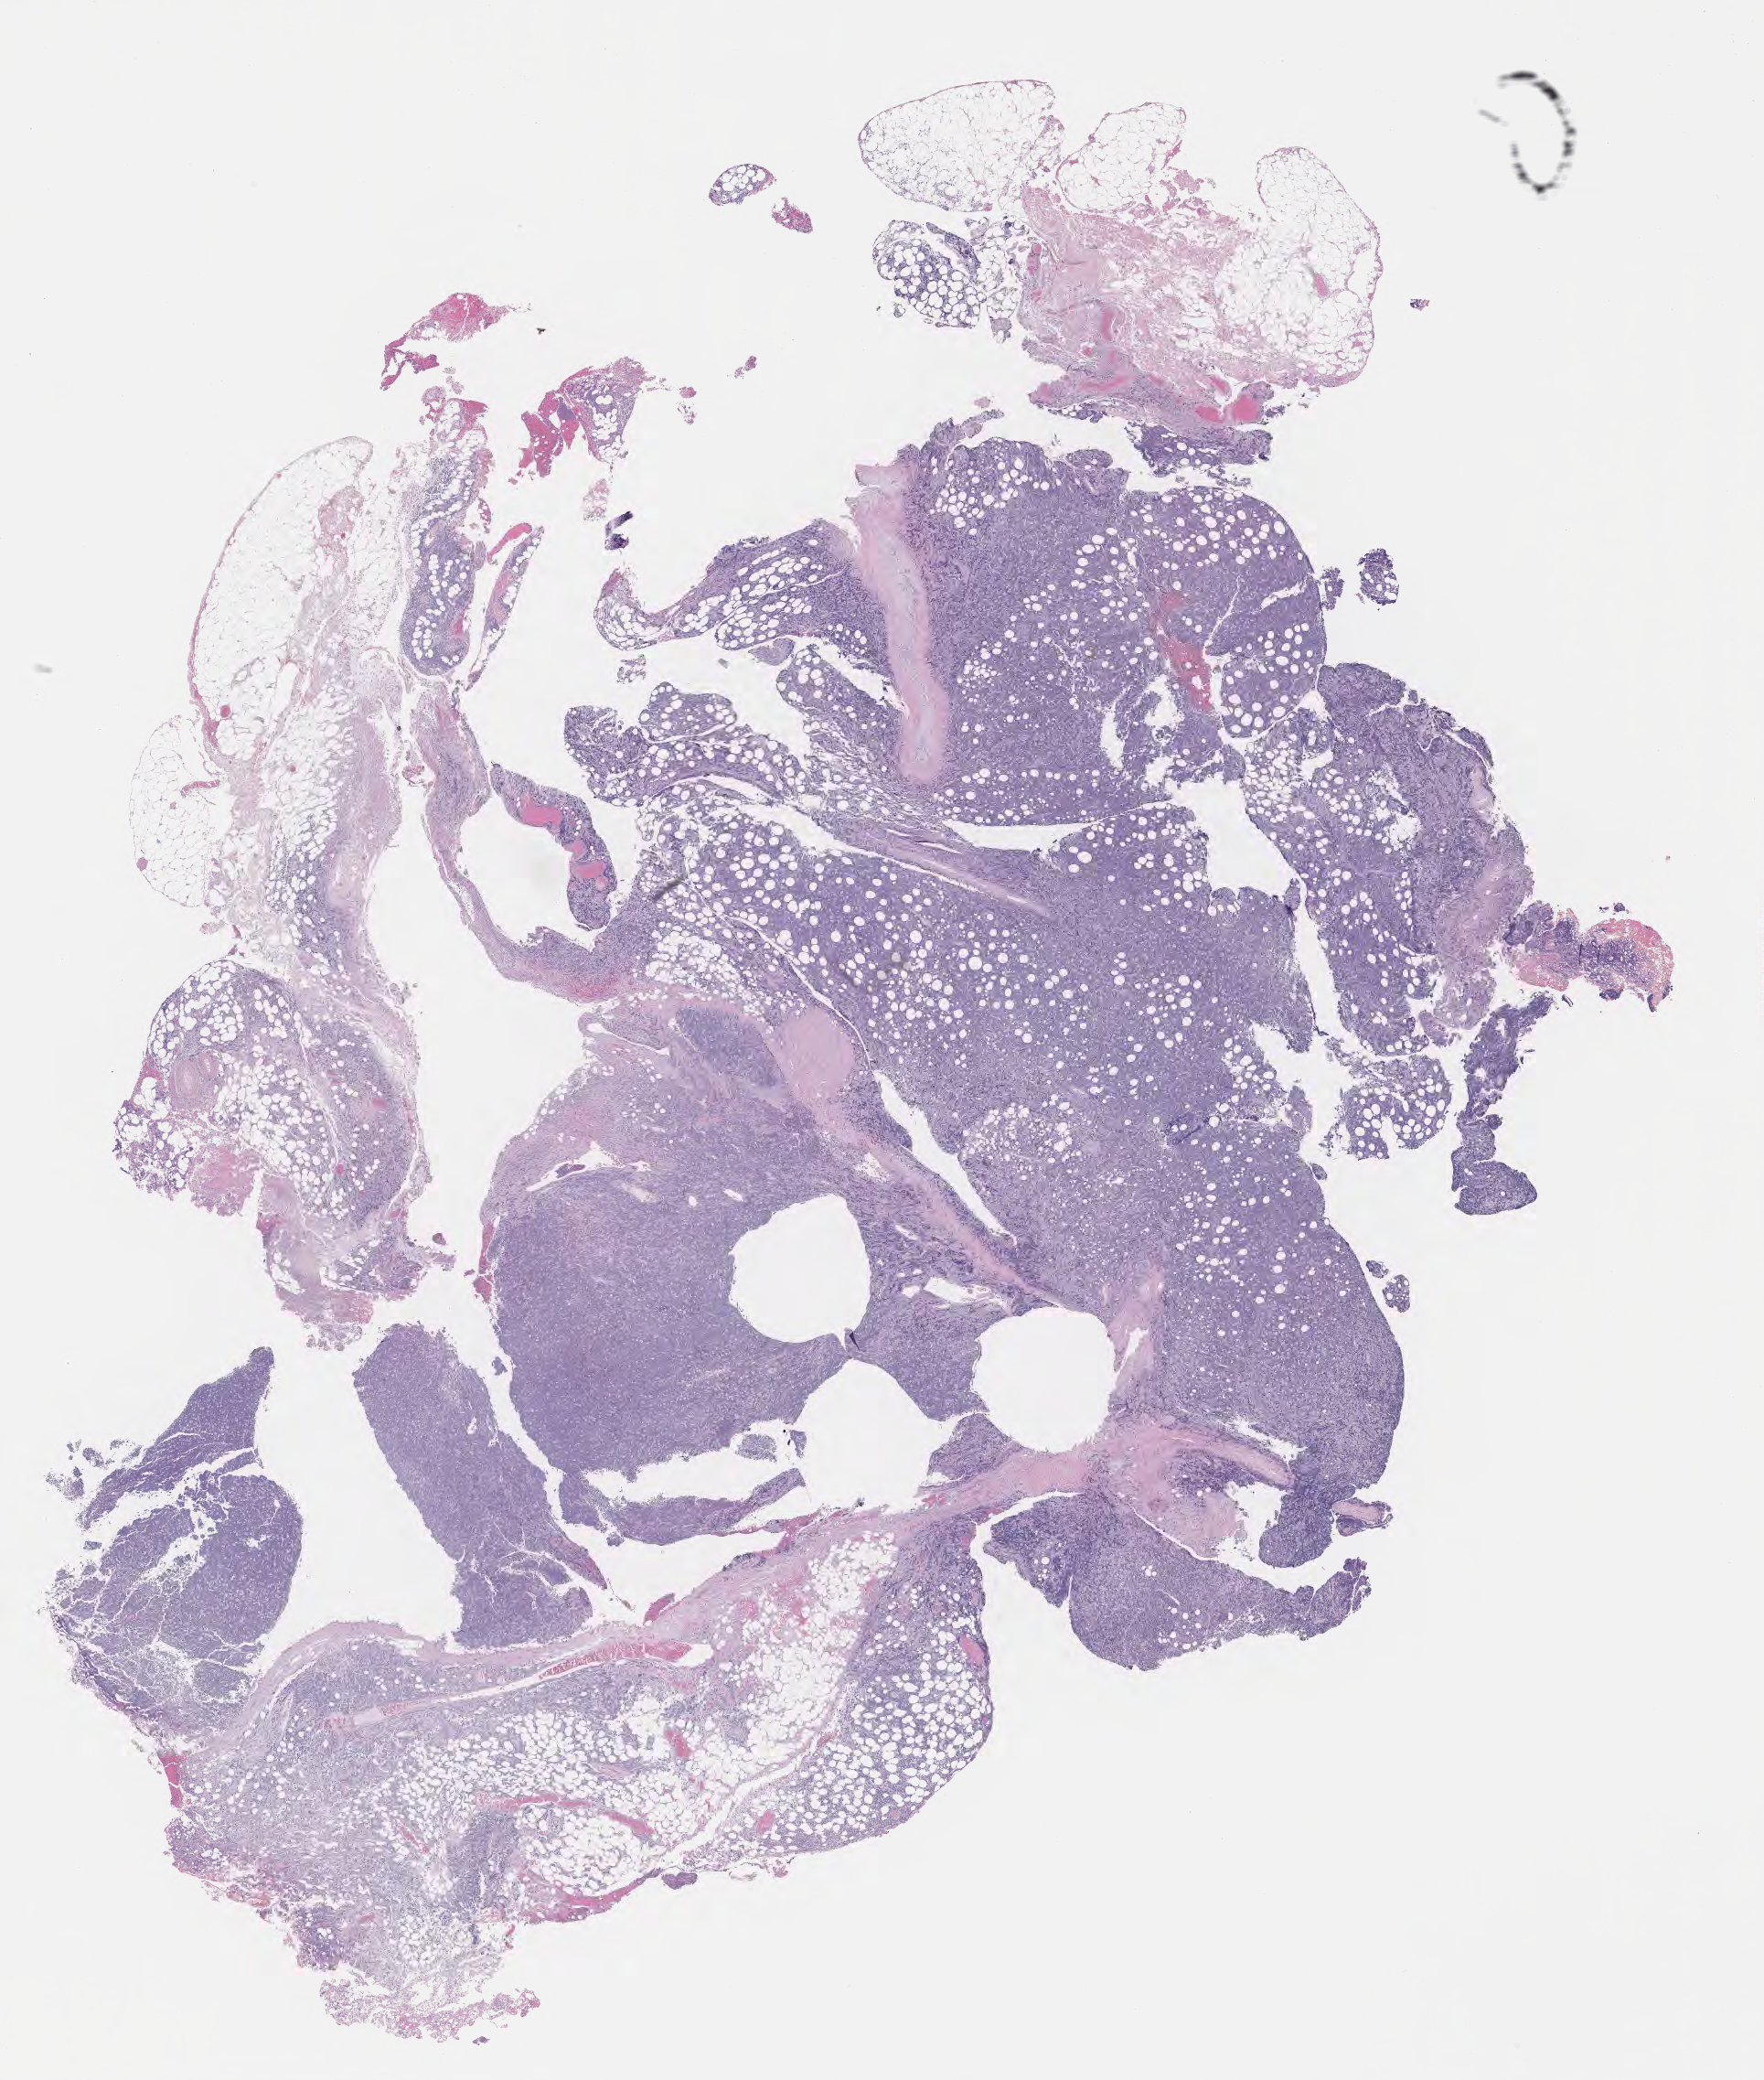
Digitized H&E-stained section — shown as a low-resolution overview of the whole scanned area (about 15.6 x 18.4 mm). Specimen: tumor tissue. Patient: female, aged 77.
Histologic diagnosis: Neoplasm, uncertain whether benign or malignant.